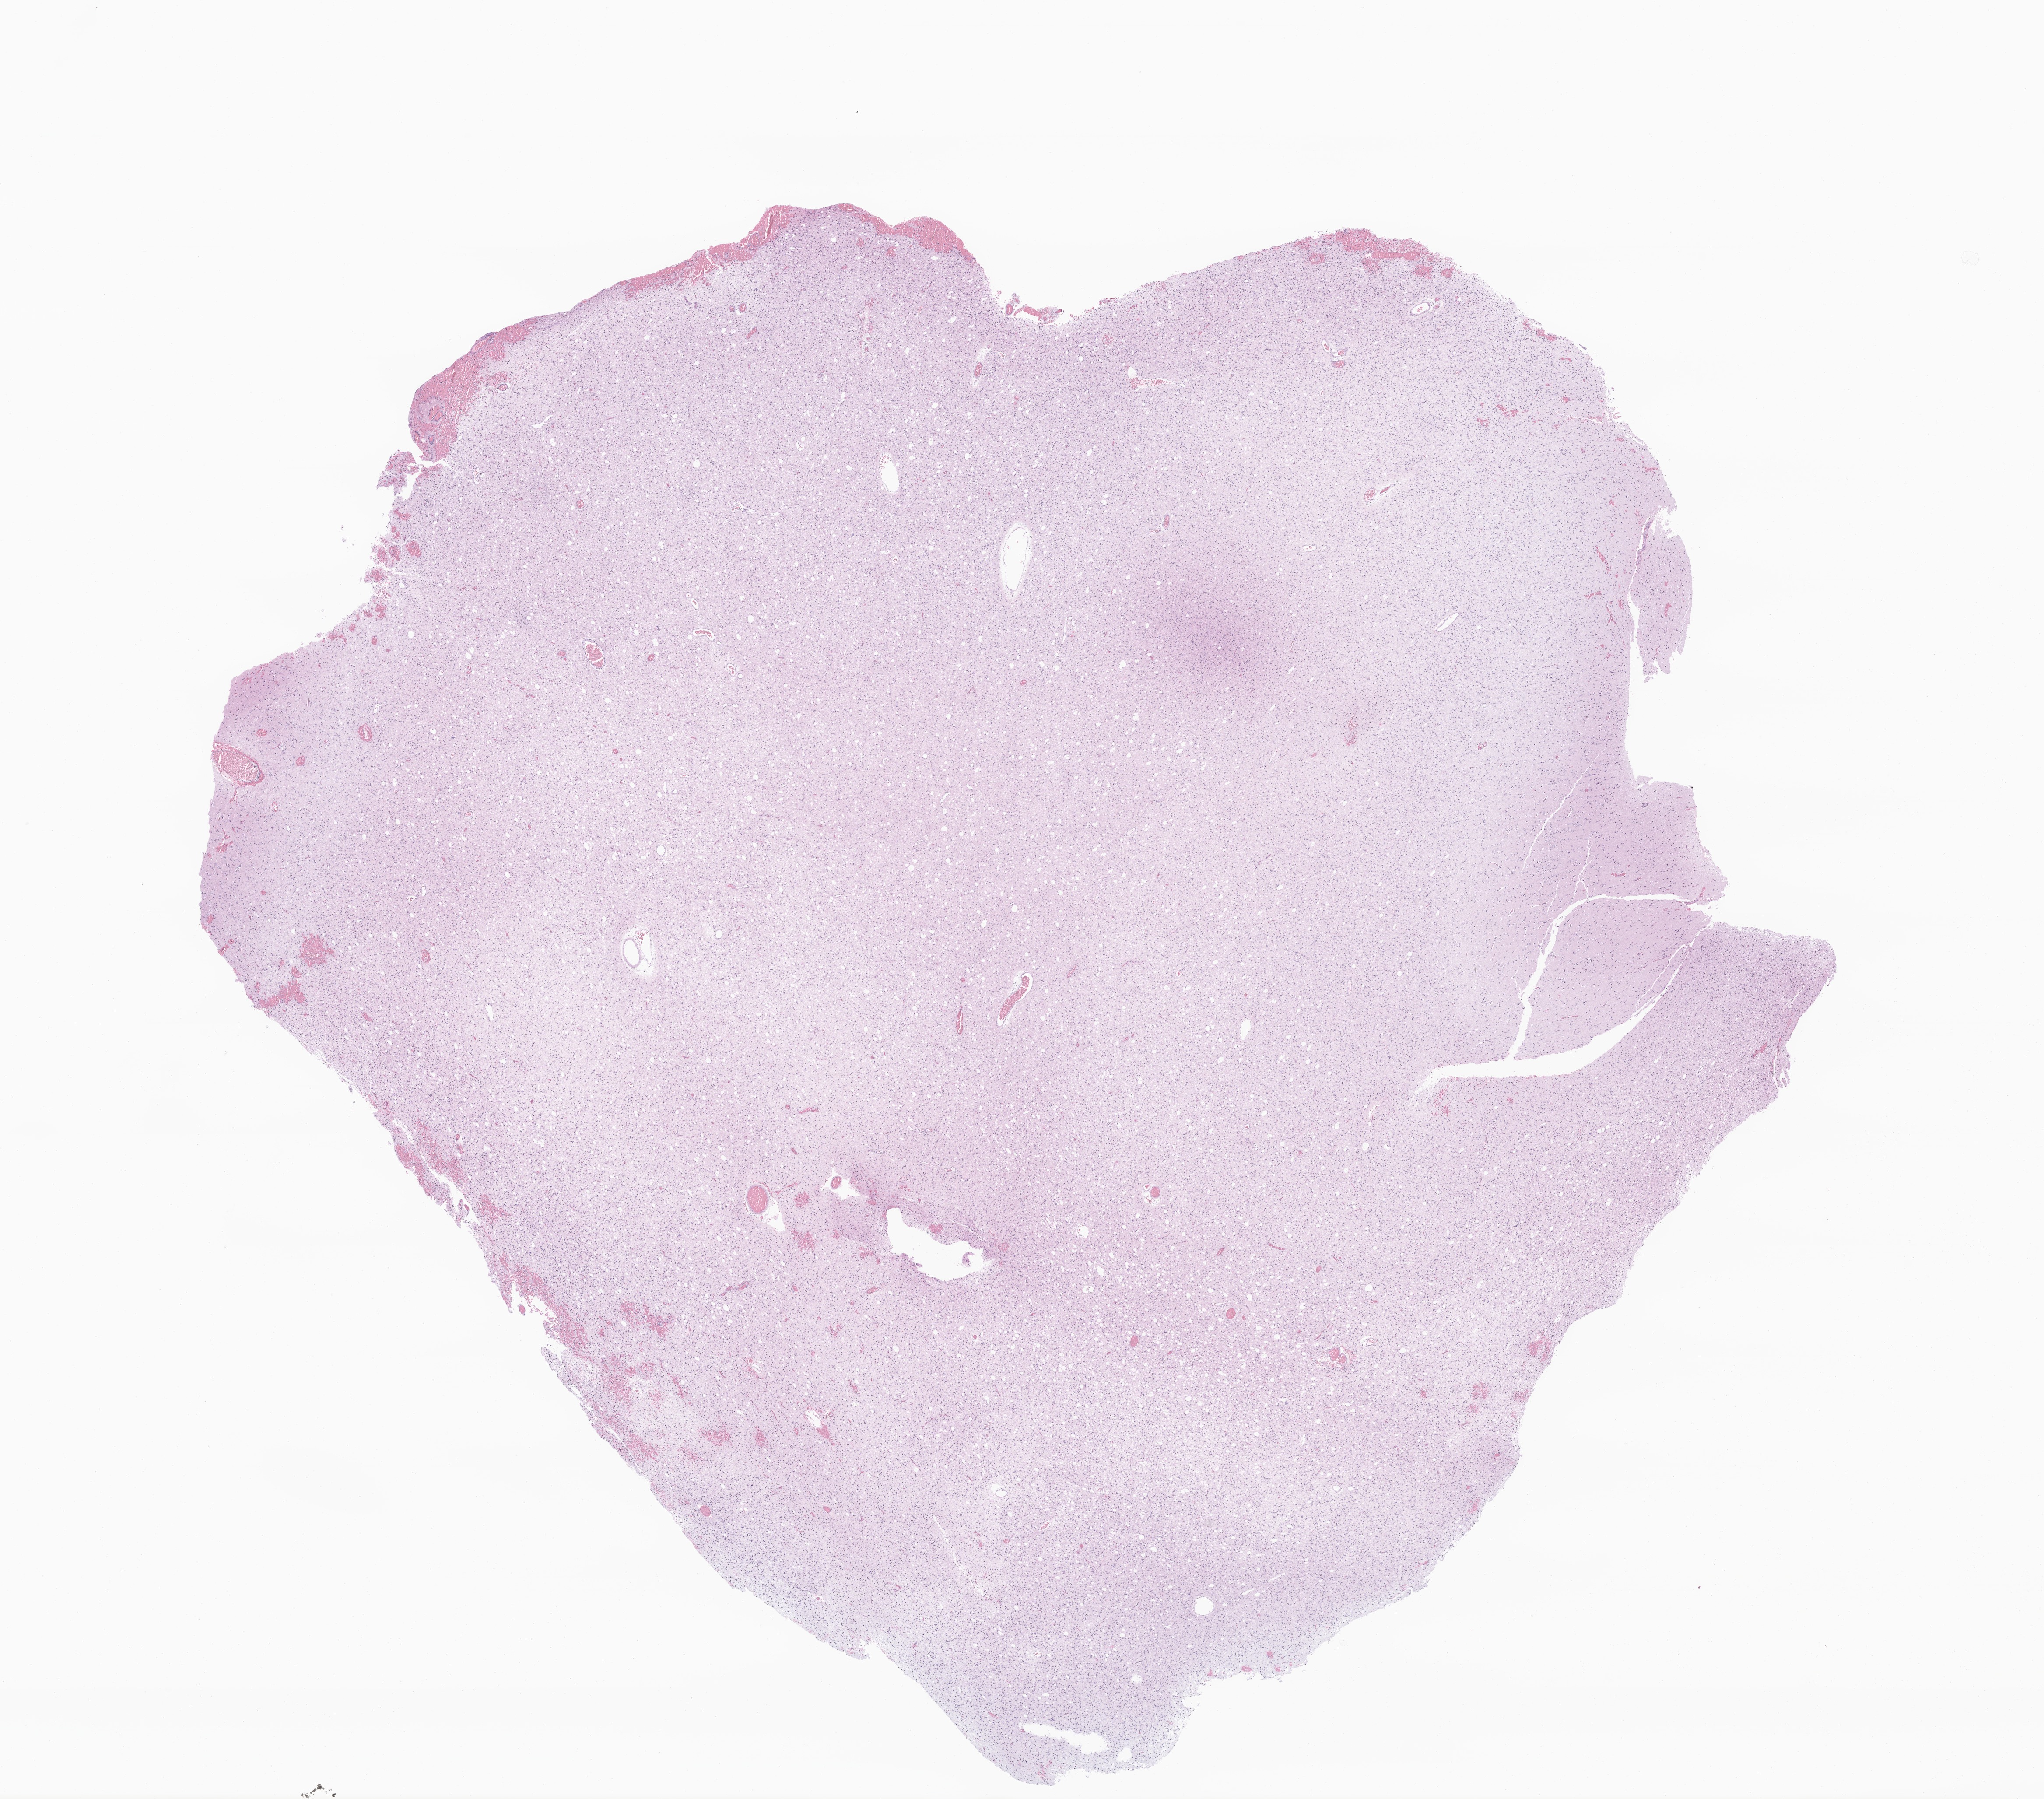
Whole-slide image, haematoxylin and eosin stain of tumor tissue from the brain — a low-resolution overview of the entire scanned area, about 19.7 x 17.3 mm. Formalin-fixed, paraffin-embedded (FFPE) tissue. Patient male; age 246 months (20 years 6 months).
- recorded diagnosis: Astrocytoma, NOS